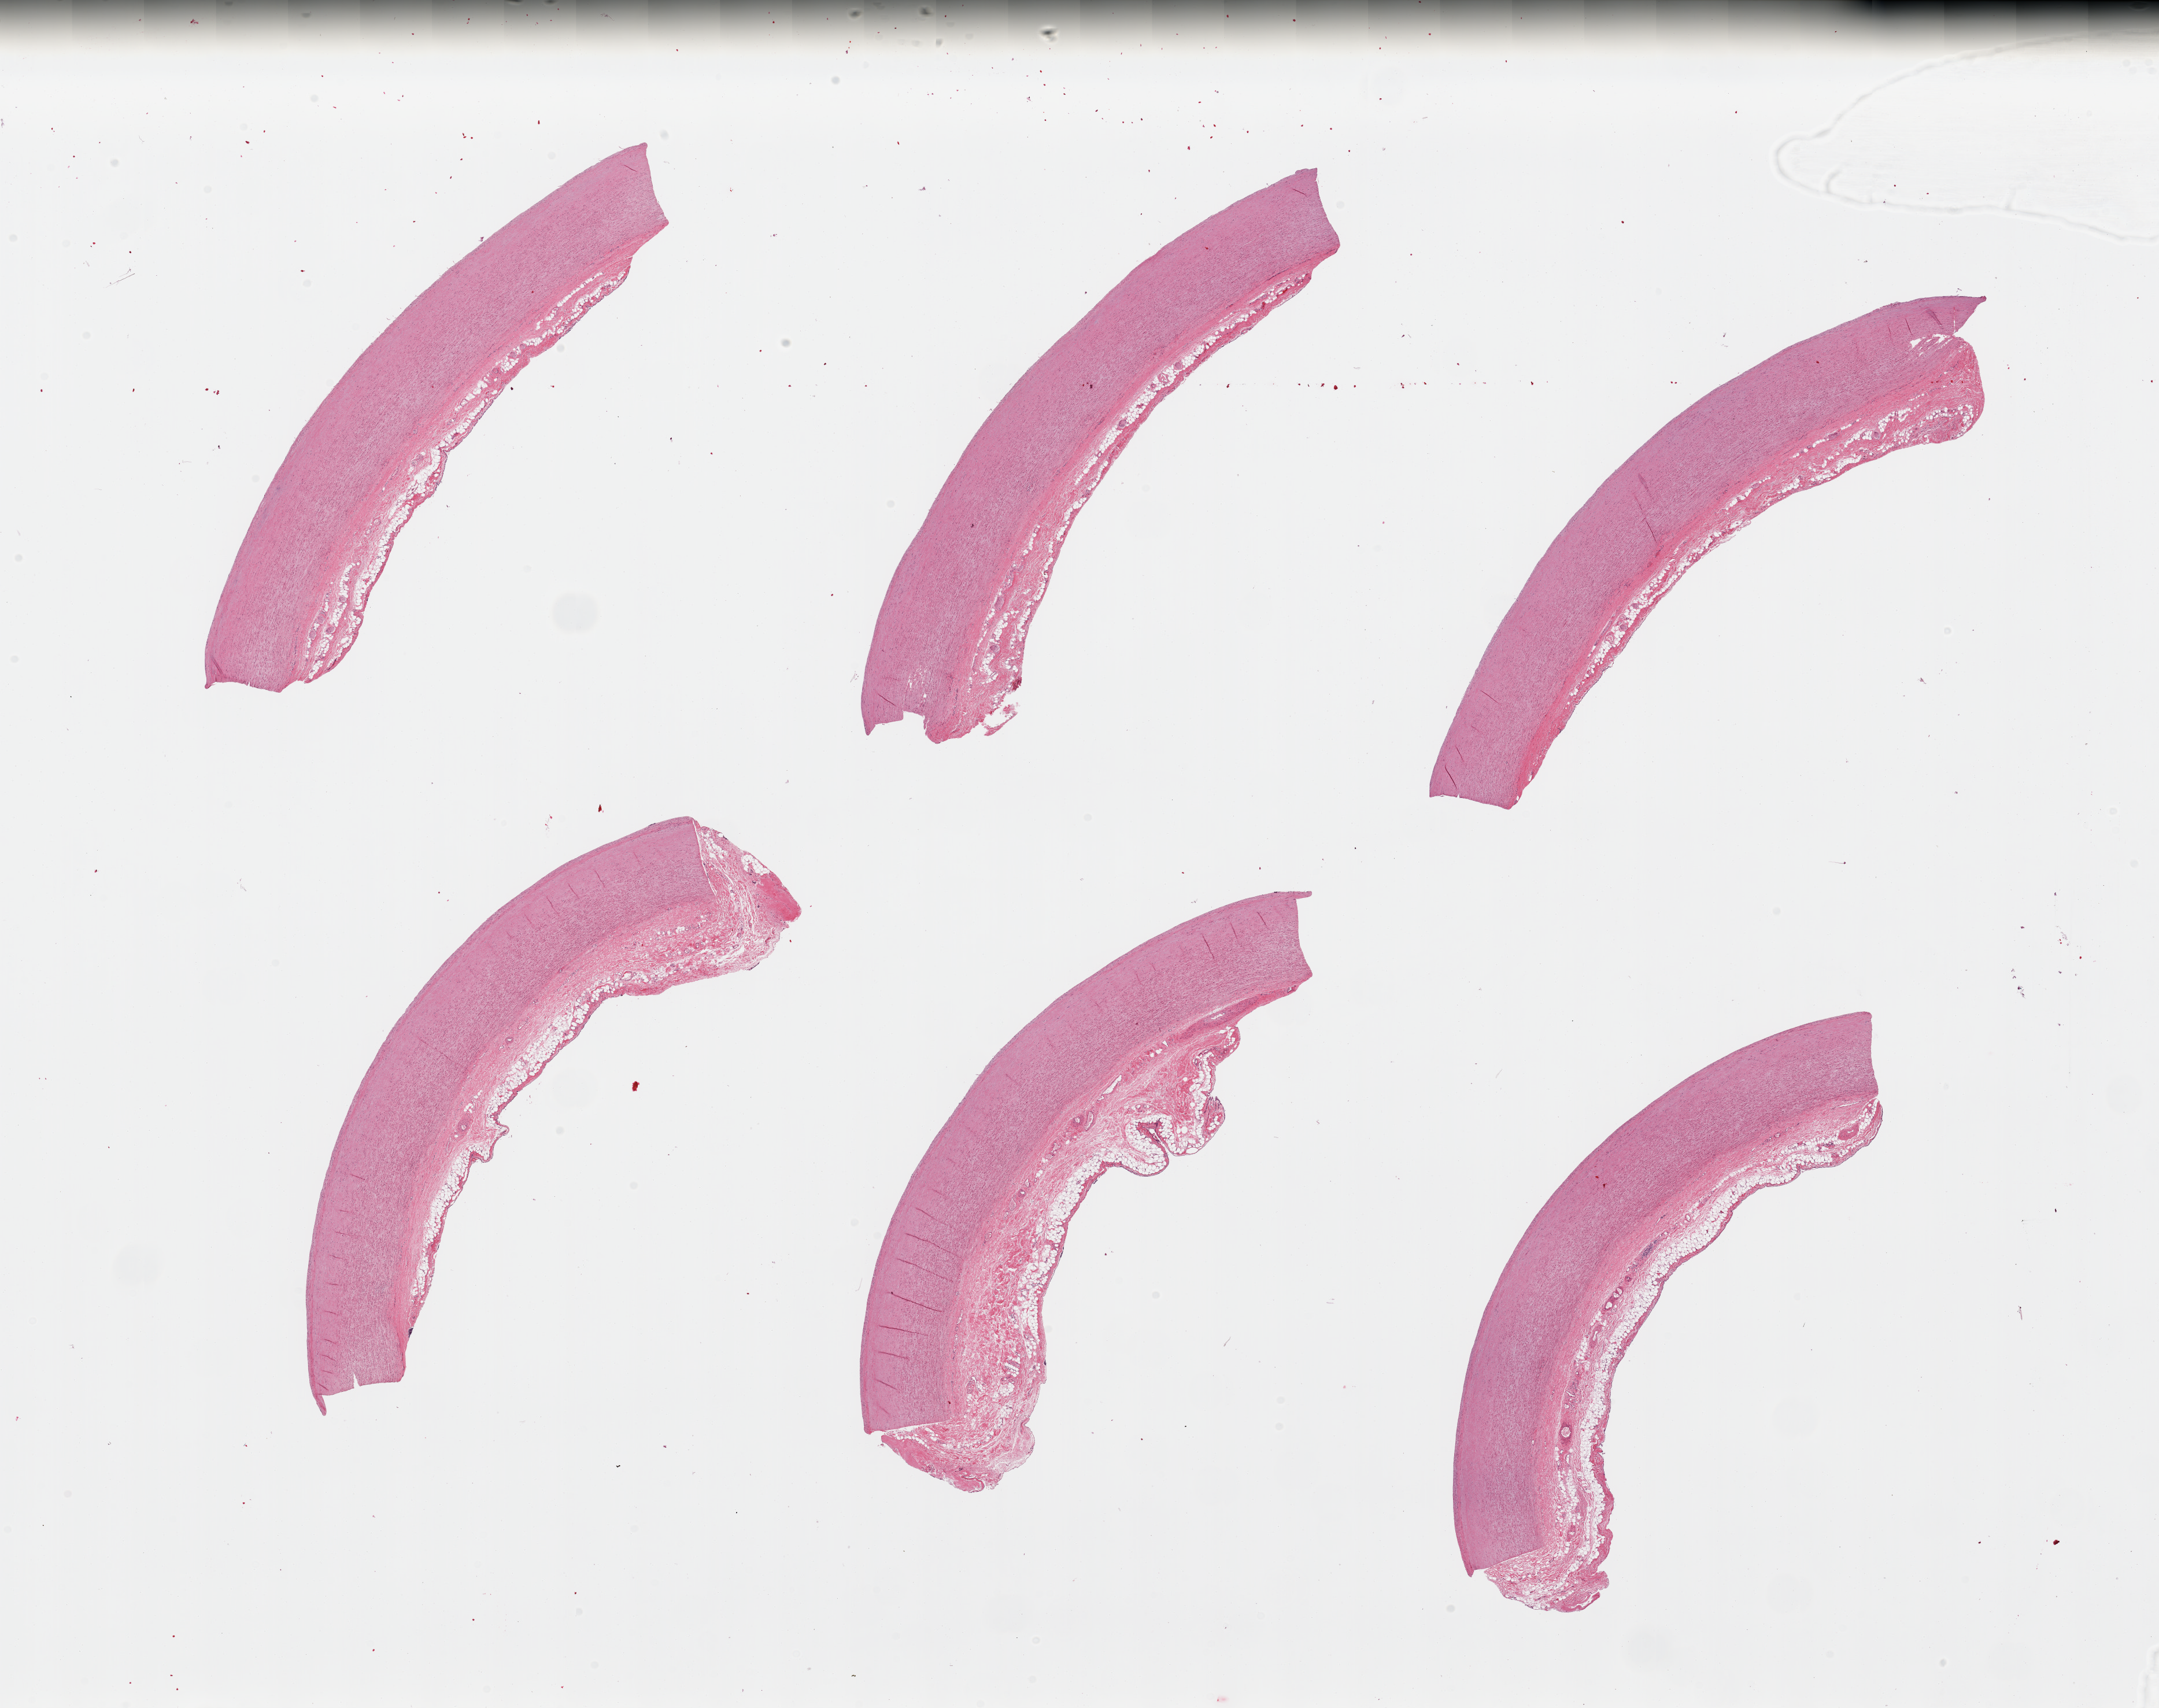
Digitized H&E-stained section, brightfield, whole scanned area (about 29.5 x 23.4 mm) shown as a low-resolution overview, PAXgene-fixed paraffin-embedded (PFPE) section, target tissue: aorta, tissue donor sample.
- reviewer comment on this tissue sample: 6 pieces, adherent serosa/fat/vasa vasorum, /`0.5-1mm thick